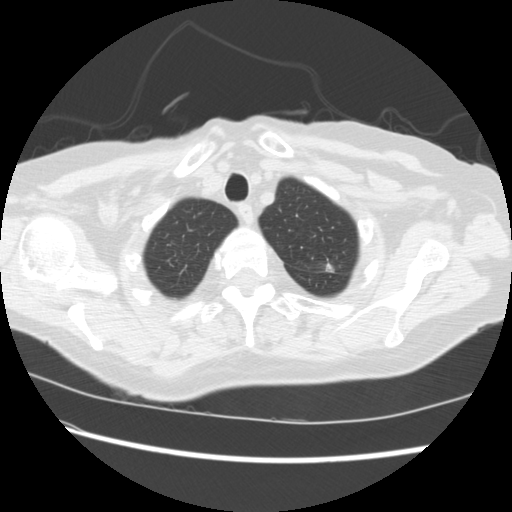
Low-dose screening chest CT, one axial slice; position 193 of 224 along the scan axis; 120 kVp; lung window (W 1500 / L -600 HU); 512 × 512 image matrix, field of view 340 × 340 mm.
Annotated regions visible in this slice (expert manual segmentation):
- lesion 1 (tumor, upper lobe of left lung): bounding box (x1, y1, x2, y2) in pixels: (326, 265, 333, 272)